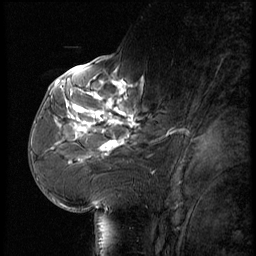
Breast MRI (dynamic contrast-enhanced), one sagittal slice; slice 28 of 56 in the series (ordered by position); dynamic contrast-enhanced series, image 2 of 3 at this slice position (ordered by acquisition); 1.5 T; TE 4.2 ms, TR 9 ms; 256 × 256 image matrix, field of view 180 × 180 mm. Patient: female, 61 years. Case-level facts recorded for this patient, not image findings: setting: breast cancer imaged before/during neoadjuvant chemotherapy; receptor status: HR-positive, HER2-negative.
Annotated regions visible in this slice (semi-automatic segmentation, software-assisted and operator-edited):
- analysis volume of interest (the breast-tissue region the enhancement analysis was run in; not a lesion): bounding box [x1, y1, x2, y2] px = [65, 74, 172, 175]
- tumour enhancement mask (voxels above the 140 % enhancement threshold inside the analysis volume of interest): [71, 78, 143, 153]